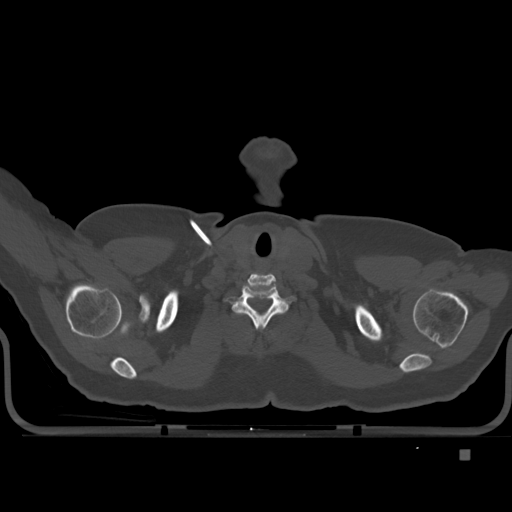
CT including the spine, one axial slice; slice 411 of 477 in the series (ordered by position); bone window (W 1800 / L 400 HU); 1.5 mm slice thickness; 512 × 512 image matrix, field of view 422 × 422 mm. Patient: female, 74 years. Case-level facts recorded for this patient, not image findings: primary cancer: colon.
Structures marked on this image (semi-automatic segmentation, software-assisted and operator-edited):
- T1 vertebra: box from (x=255, y=308) to (x=281, y=327) px